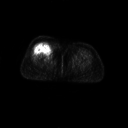
FDG PET of an extremity soft-tissue mass (from a PET/CT study), one axial slice; position 29 of 267 along the scan axis; 3.27 mm slice thickness; 128 × 128 image matrix, field of view 700 × 700 mm. Patient: female, 56 years. Case-level facts recorded for this patient, not image findings: histological type: malignant solitary fibrous tumor; grade: intermediate; site of the primary tumour: right thigh.
Structures marked on this image (expert contour drawn on MRI and transferred to this co-registered scan by the dataset authors):
- gross tumour volume including surrounding oedema: box from (x=35, y=41) to (x=55, y=57) px
- gross tumour volume (mass): (x=36, y=41)–(x=54, y=56)